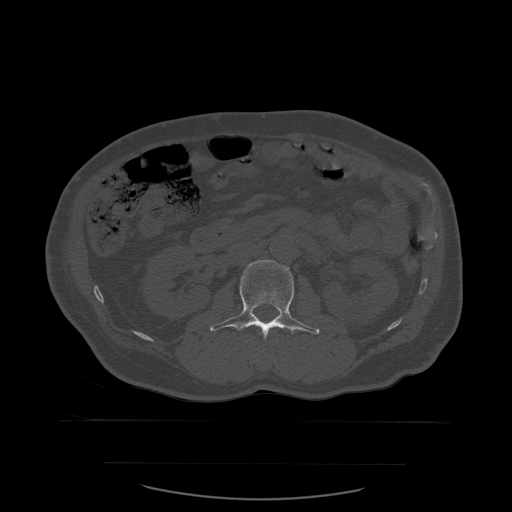
CT including the spine, one axial slice. Slice 221 of 590 in the series (ordered by position). Bone window (W 1800 / L 400 HU). 1.25 mm slice thickness. 512 × 512 image matrix. Patient age 71 years. Case-level facts recorded for this patient, not image findings: primary cancer: lung; vertebrae with lytic lesions (as recorded): T1, T2, L5, S1.
Annotated regions visible in this slice (semi-automatic segmentation, software-assisted and operator-edited):
- L2 vertebra: bounding box (x1, y1, x2, y2) in pixels: (210, 260, 320, 340)